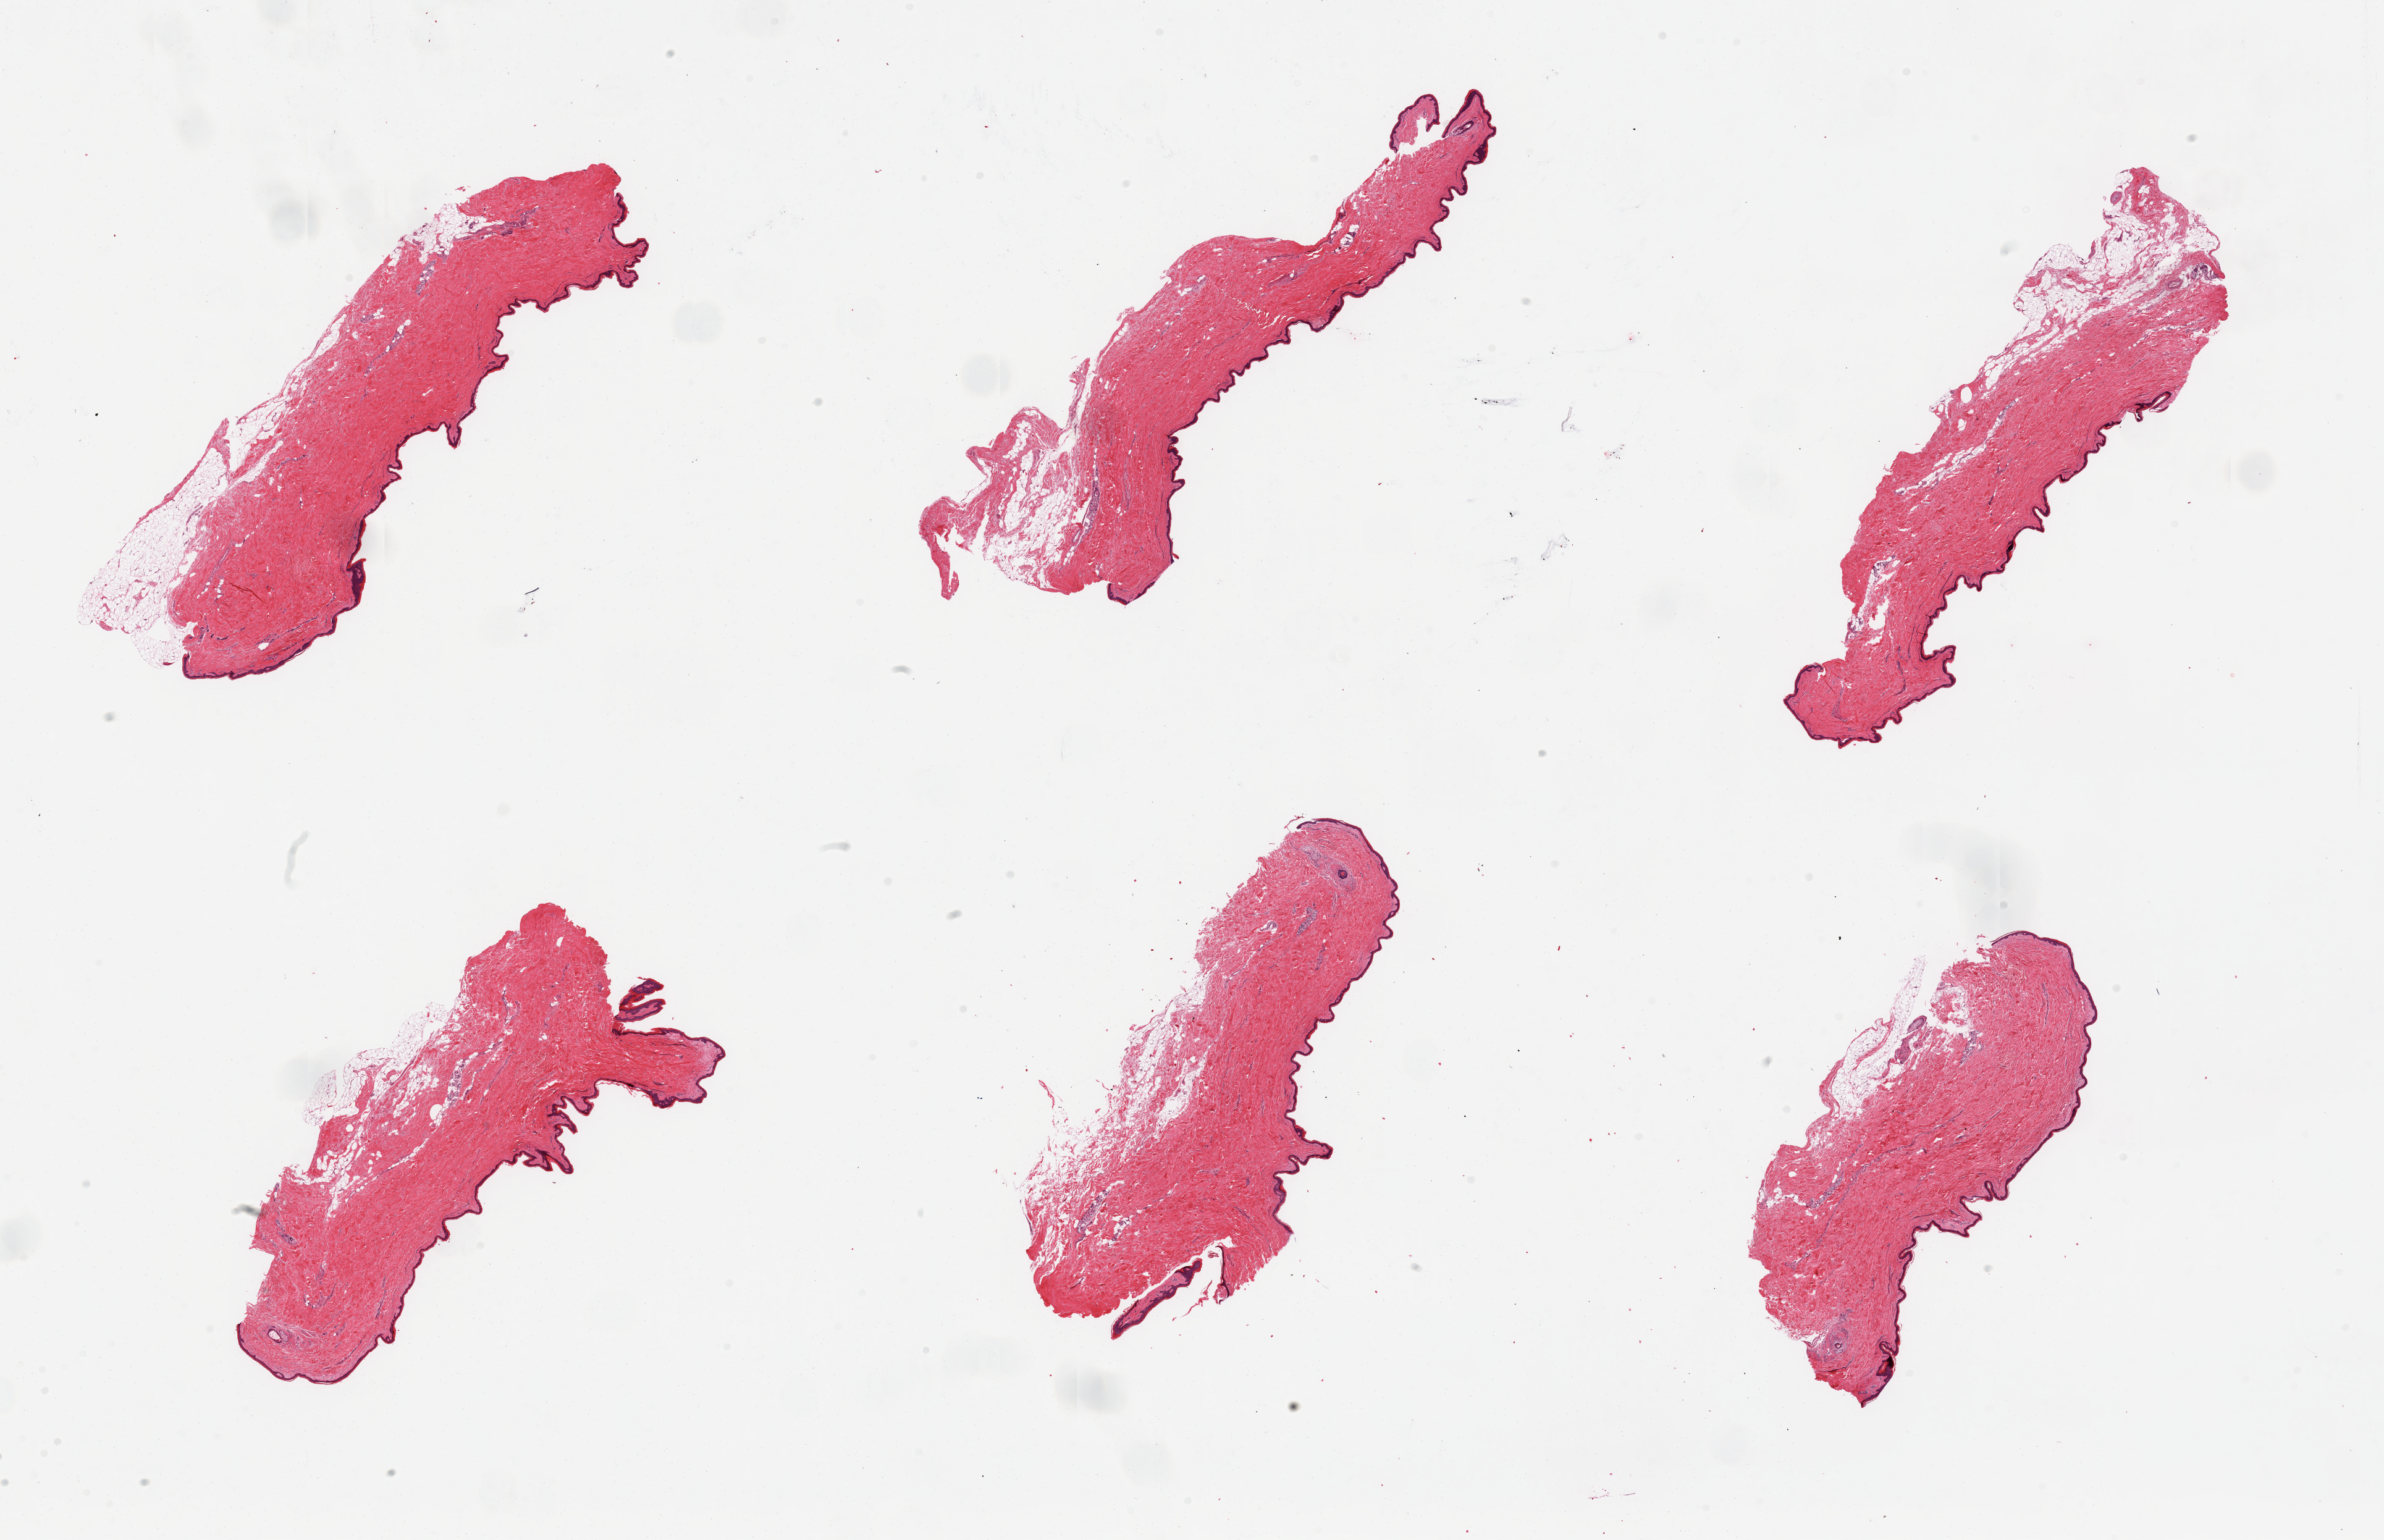
Whole-slide image, hematoxylin and eosin (H&E) stain, a low-resolution overview of the entire scanned area, about 30.5 x 19.7 mm (acquisition: 20x scan); PAXgene-fixed paraffin-embedded (PFPE) section; sampled site (target tissue): skin of suprapubic region; tissue donor sample.
Reviewer comment on this tissue sample: 6 pieces.